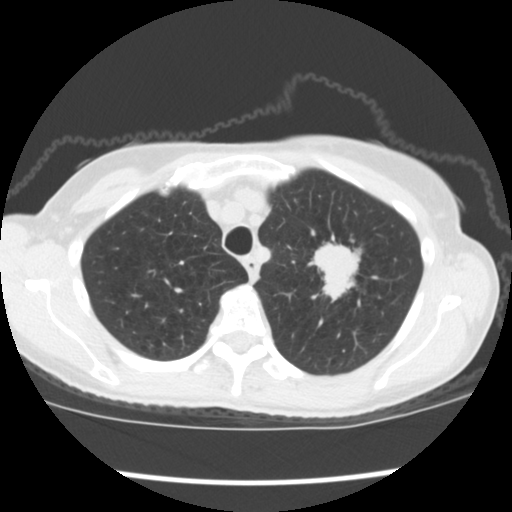
Low-dose screening chest CT, axial slice, baseline screening round, lung window (W 1500 / L -600 HU), slice 30 of 176 in the series, 512 × 512 image matrix. Female, age 67 years at enrolment. Former smoker at enrolment.
Expert reader's lesion annotation, bounding box [x1, y1, x2, y2] px = [304, 235, 376, 310]. Screening reader's record for this exam (one nodule recorded; not confirmed to be the boxed lesion): non-calcified nodule or mass ≥4 mm, left upper lobe, 34 × 32 mm, spiculated (stellate) margins, soft tissue attenuation, pre-existing on the prior screen: no.